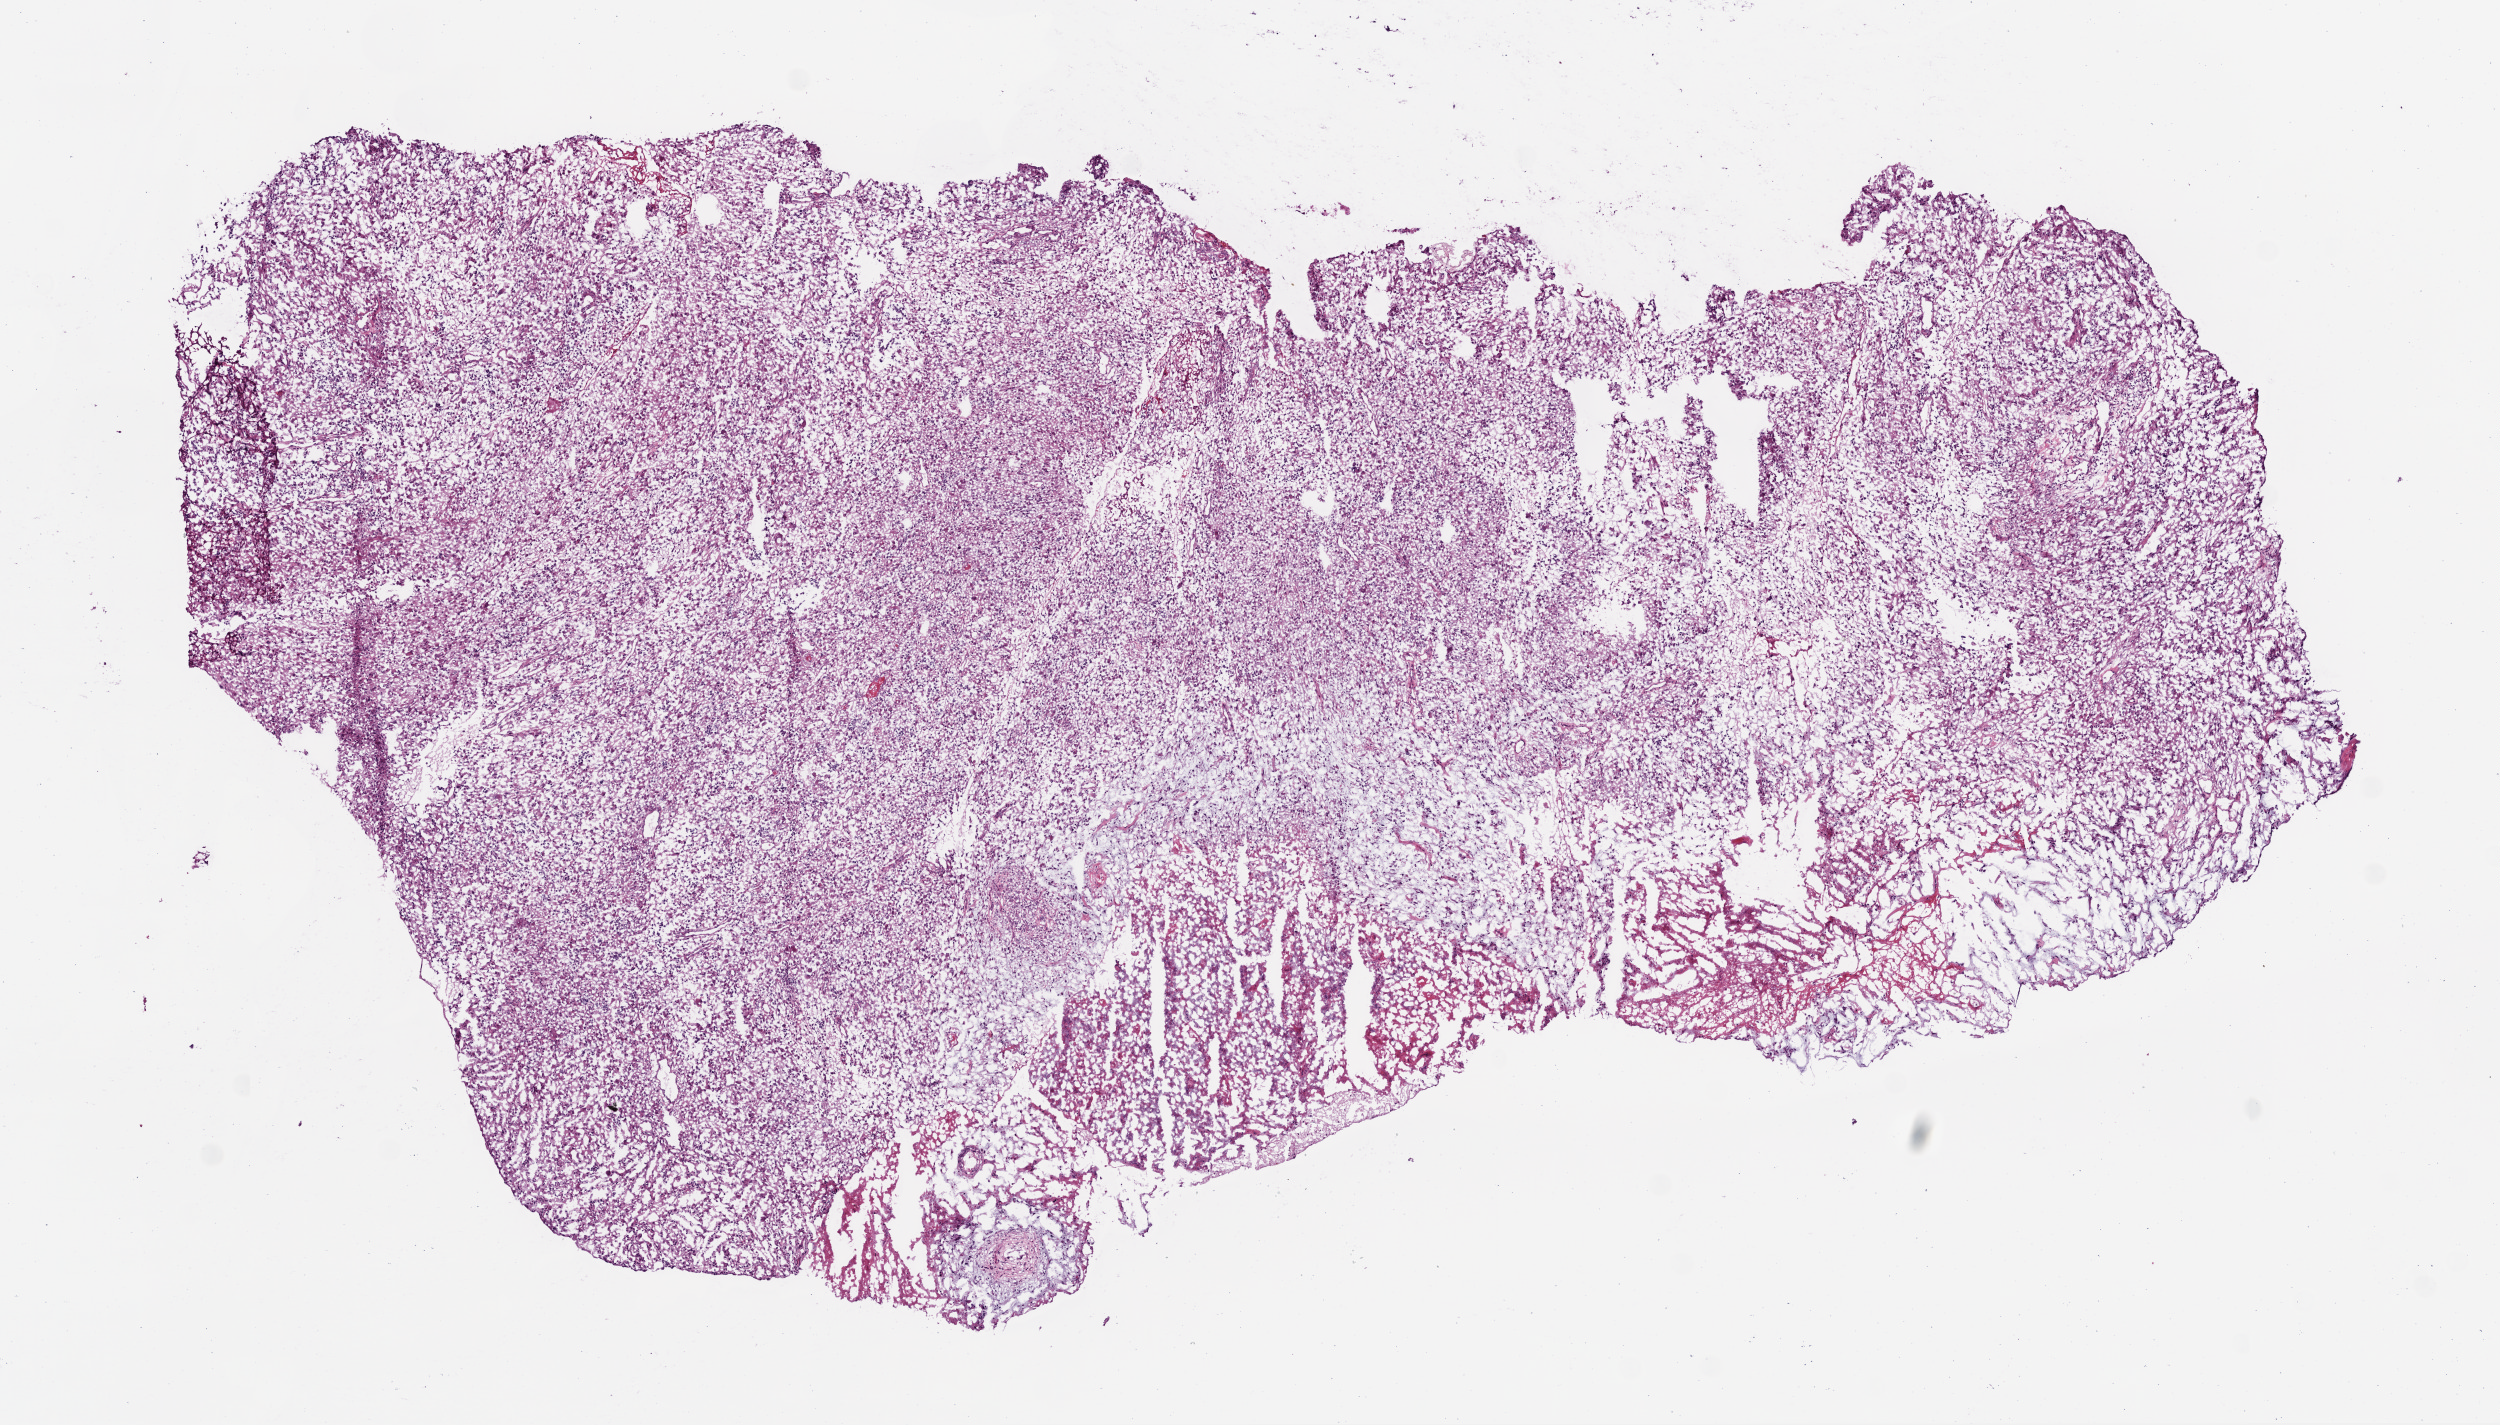
H&E-stained whole-slide image, shown as a low-resolution overview of the whole scanned area (about 10.0 x 5.7 mm). Frozen section from the bottom of the tissue portion. Brain, primary tumour sample. Female, age 47 years at initial diagnosis. Slide review estimates, as recorded: tumour cells 98%, tumour nuclei 75%, normal cells 0%, stromal cells 0%, necrosis 2%.
- diagnosis: Glioblastoma